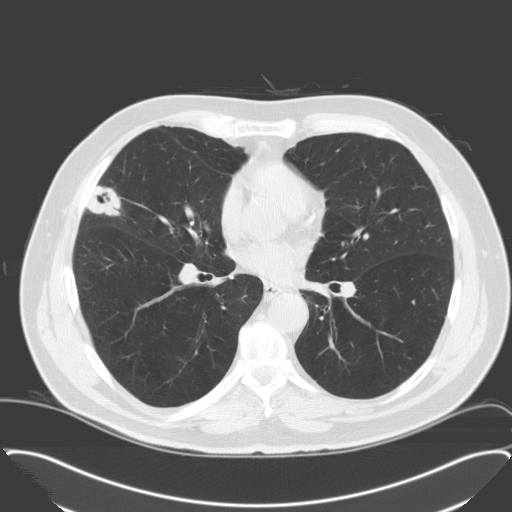
Chest CT (low-dose screening protocol), one axial image, third annual screen, lung window (W 1500 / L -600 HU), standard (soft-tissue) reconstruction kernel (C), slice 86 of 174 in the series. Male participant, aged 65 years at enrolment. Former smoker at enrolment.
- Expert-annotated lung lesion, bounding box <70,177,130,232> (left, top, right, bottom; pixels).
- Screening reader's record for this exam (one nodule recorded; not confirmed to be the boxed lesion): non-calcified nodule or mass ≥4 mm, right middle lobe, 28 × 23 mm, spiculated (stellate) margins, soft tissue attenuation, pre-existing on the prior screen: no.
- Official screen result: positive, other.
- Participant outcome: lung cancer diagnosed 25 days after this screen — adenocarcinoma, NOS, right middle lobe, moderately differentiated (G2), stage IA (AJCC 6th edition), 25 mm at pathology.